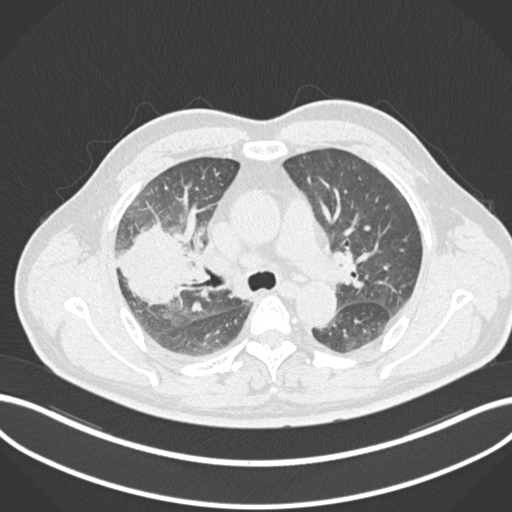
Chest CT, one axial slice. Position 652 of 852 along the scan axis. Reconstruction kernel B30f. Lung window (W 1500 / L -600 HU). 1 mm slice thickness. 512 × 512 image matrix, field of view 400 × 400 mm. Male patient, age 55 years. Case-level facts recorded for this patient, not image findings: clinical TNM (as recorded): T3 N2 M1.
Outlined on this slice (rectangle marked by the reading radiologist):
- lung tumour (recorded histology: adenocarcinoma): box from (x=115, y=216) to (x=200, y=307) px